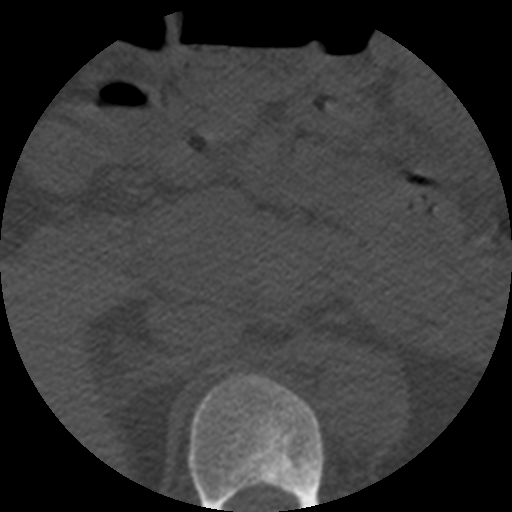
CT including the spine, one axial slice; slice 237 of 508 in the series (ordered by position); reconstruction kernel STANDARD; 120 kVp; bone window (W 1800 / L 400 HU); 1.25 mm slice thickness; 512 × 512 image matrix. Patient age 57 years. From the clinical record (not read from this slice): primary cancer: prostate.
Outlined on this slice (semi-automatic segmentation, software-assisted and operator-edited):
- T11 vertebra: box from (x=188, y=374) to (x=324, y=512) px